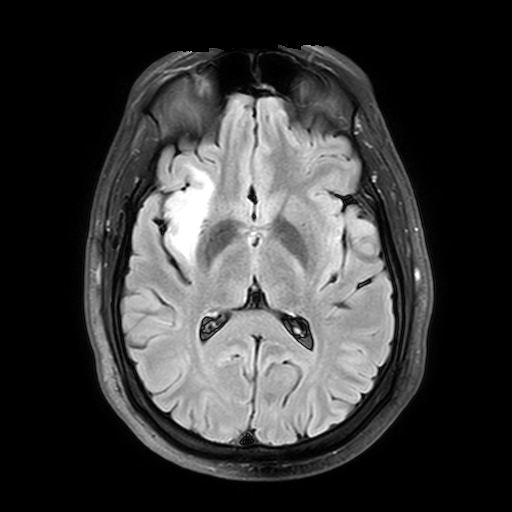
Brain MRI from a brain-tumour surgery series, one axial slice; slice 21 of 42 in the series (ordered by position); T2 FLAIR; 4 mm slice thickness; 512 × 512 image matrix, field of view 240 × 240 mm. Case-level facts recorded for this patient, not image findings: histopathology: Astrocytoma; WHO grade: 2; IDH mutation: yes.
Outlined on this slice (expert manual segmentation):
- tumour: box from (x=137, y=167) to (x=223, y=260) px